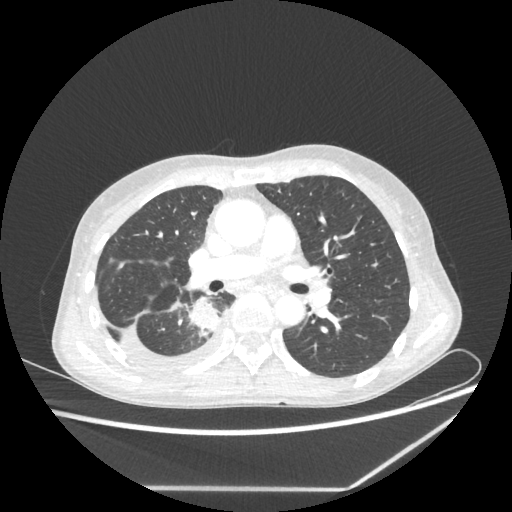
Chest CT, one axial slice; slice 131 of 237 in the series (ordered by position); 80 kVp; lung window (W 1500 / L -600 HU); 512 × 512 image matrix, field of view 364 × 364 mm. Patient: female, 59 years. Case-level facts recorded for this patient, not image findings: clinical TNM (as recorded): T1c N1 M1.
Outlined on this slice (rectangle marked by the reading radiologist):
- lung tumour (recorded histology: adenocarcinoma): box from (x=187, y=295) to (x=224, y=338) px